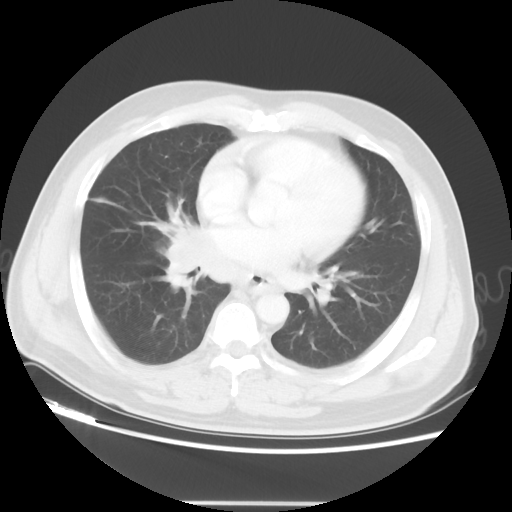
Chest CT, one axial slice; slice 23 of 48 in the series (ordered by position); 120 kVp; lung window (W 1500 / L -600 HU); 5 mm slice thickness; 512 × 512 image matrix, field of view 390 × 390 mm. Male patient, age 53 years. From the clinical record (not read from this slice): clinical TNM (as recorded): T2 N3 M0; histopathological grade: G3.
Outlined on this slice (rectangle marked by the reading radiologist):
- lung tumour (recorded histology: small cell carcinoma): box from (x=171, y=222) to (x=207, y=297) px